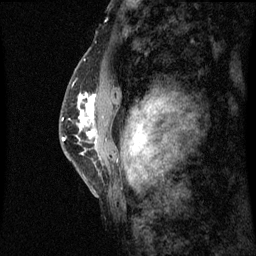
Breast MRI (dynamic contrast-enhanced), one sagittal slice. Dynamic contrast-enhanced series, image 2 of 3 at this slice position (ordered by acquisition). 1.5 T. TE 4.2 ms, TR 8.9 ms. 256 × 256 image matrix. Female patient, age 50 years. Case-level facts recorded for this patient, not image findings: setting: breast cancer imaged before/during neoadjuvant chemotherapy; receptor status: triple-negative.
Annotated regions visible in this slice (semi-automatic segmentation, software-assisted and operator-edited):
- analysis volume of interest (the breast-tissue region the enhancement analysis was run in; not a lesion): bounding box <68,80,99,169> (left, top, right, bottom; pixels)
- tumour enhancement mask (voxels above the 70 % enhancement threshold inside the analysis volume of interest): <82,96,96,135>